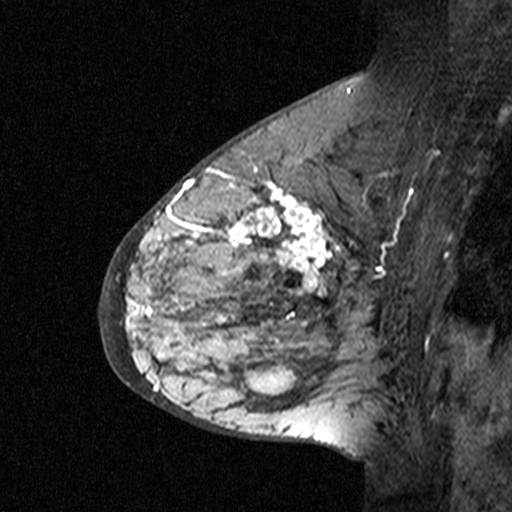
Breast MRI (dynamic contrast-enhanced), one sagittal slice. Position 22 of 44 along the scan axis. Dynamic contrast-enhanced study with each time point stored as its own series, time point 3 of 4 at this slice position (ordered by acquisition time). 1.5 T. TE 4.5 ms, TR 11 ms. 512 × 512 image matrix, field of view 200 × 200 mm. Female patient, age 65 years. Case-level facts recorded for this patient, not image findings: setting: breast cancer imaged before/during neoadjuvant chemotherapy; receptor status: HER2-positive.
Outlined on this slice (semi-automatic segmentation, software-assisted and operator-edited):
- analysis volume of interest (the breast-tissue region the enhancement analysis was run in; not a lesion): box from (x=182, y=190) to (x=353, y=361) px
- tumour enhancement mask (voxels above the 90 % enhancement threshold inside the analysis volume of interest): (x=182, y=190)–(x=331, y=327)